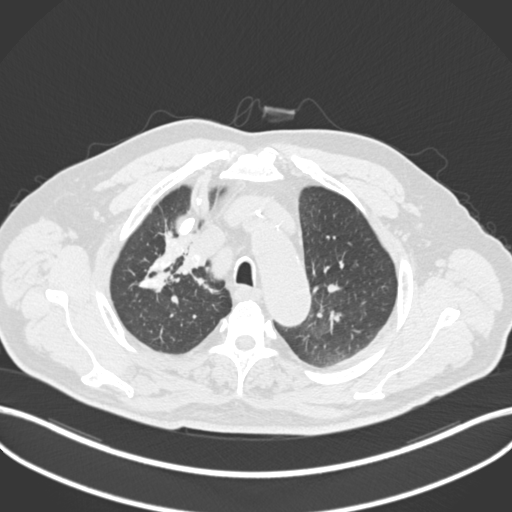
Chest CT, one axial slice; position 159 of 255 along the scan axis; reconstruction kernel B30f; 120 kVp; lung window (W 1500 / L -600 HU); 512 × 512 image matrix, field of view 400 × 400 mm. Patient: male, 60 years. From the clinical record (not read from this slice): clinical TNM (as recorded): T1b N1 M0.
Outlined on this slice (rectangle marked by the reading radiologist):
- lung tumour (recorded histology: squamous cell carcinoma): bounding box <179,243,208,279> (left, top, right, bottom; pixels)